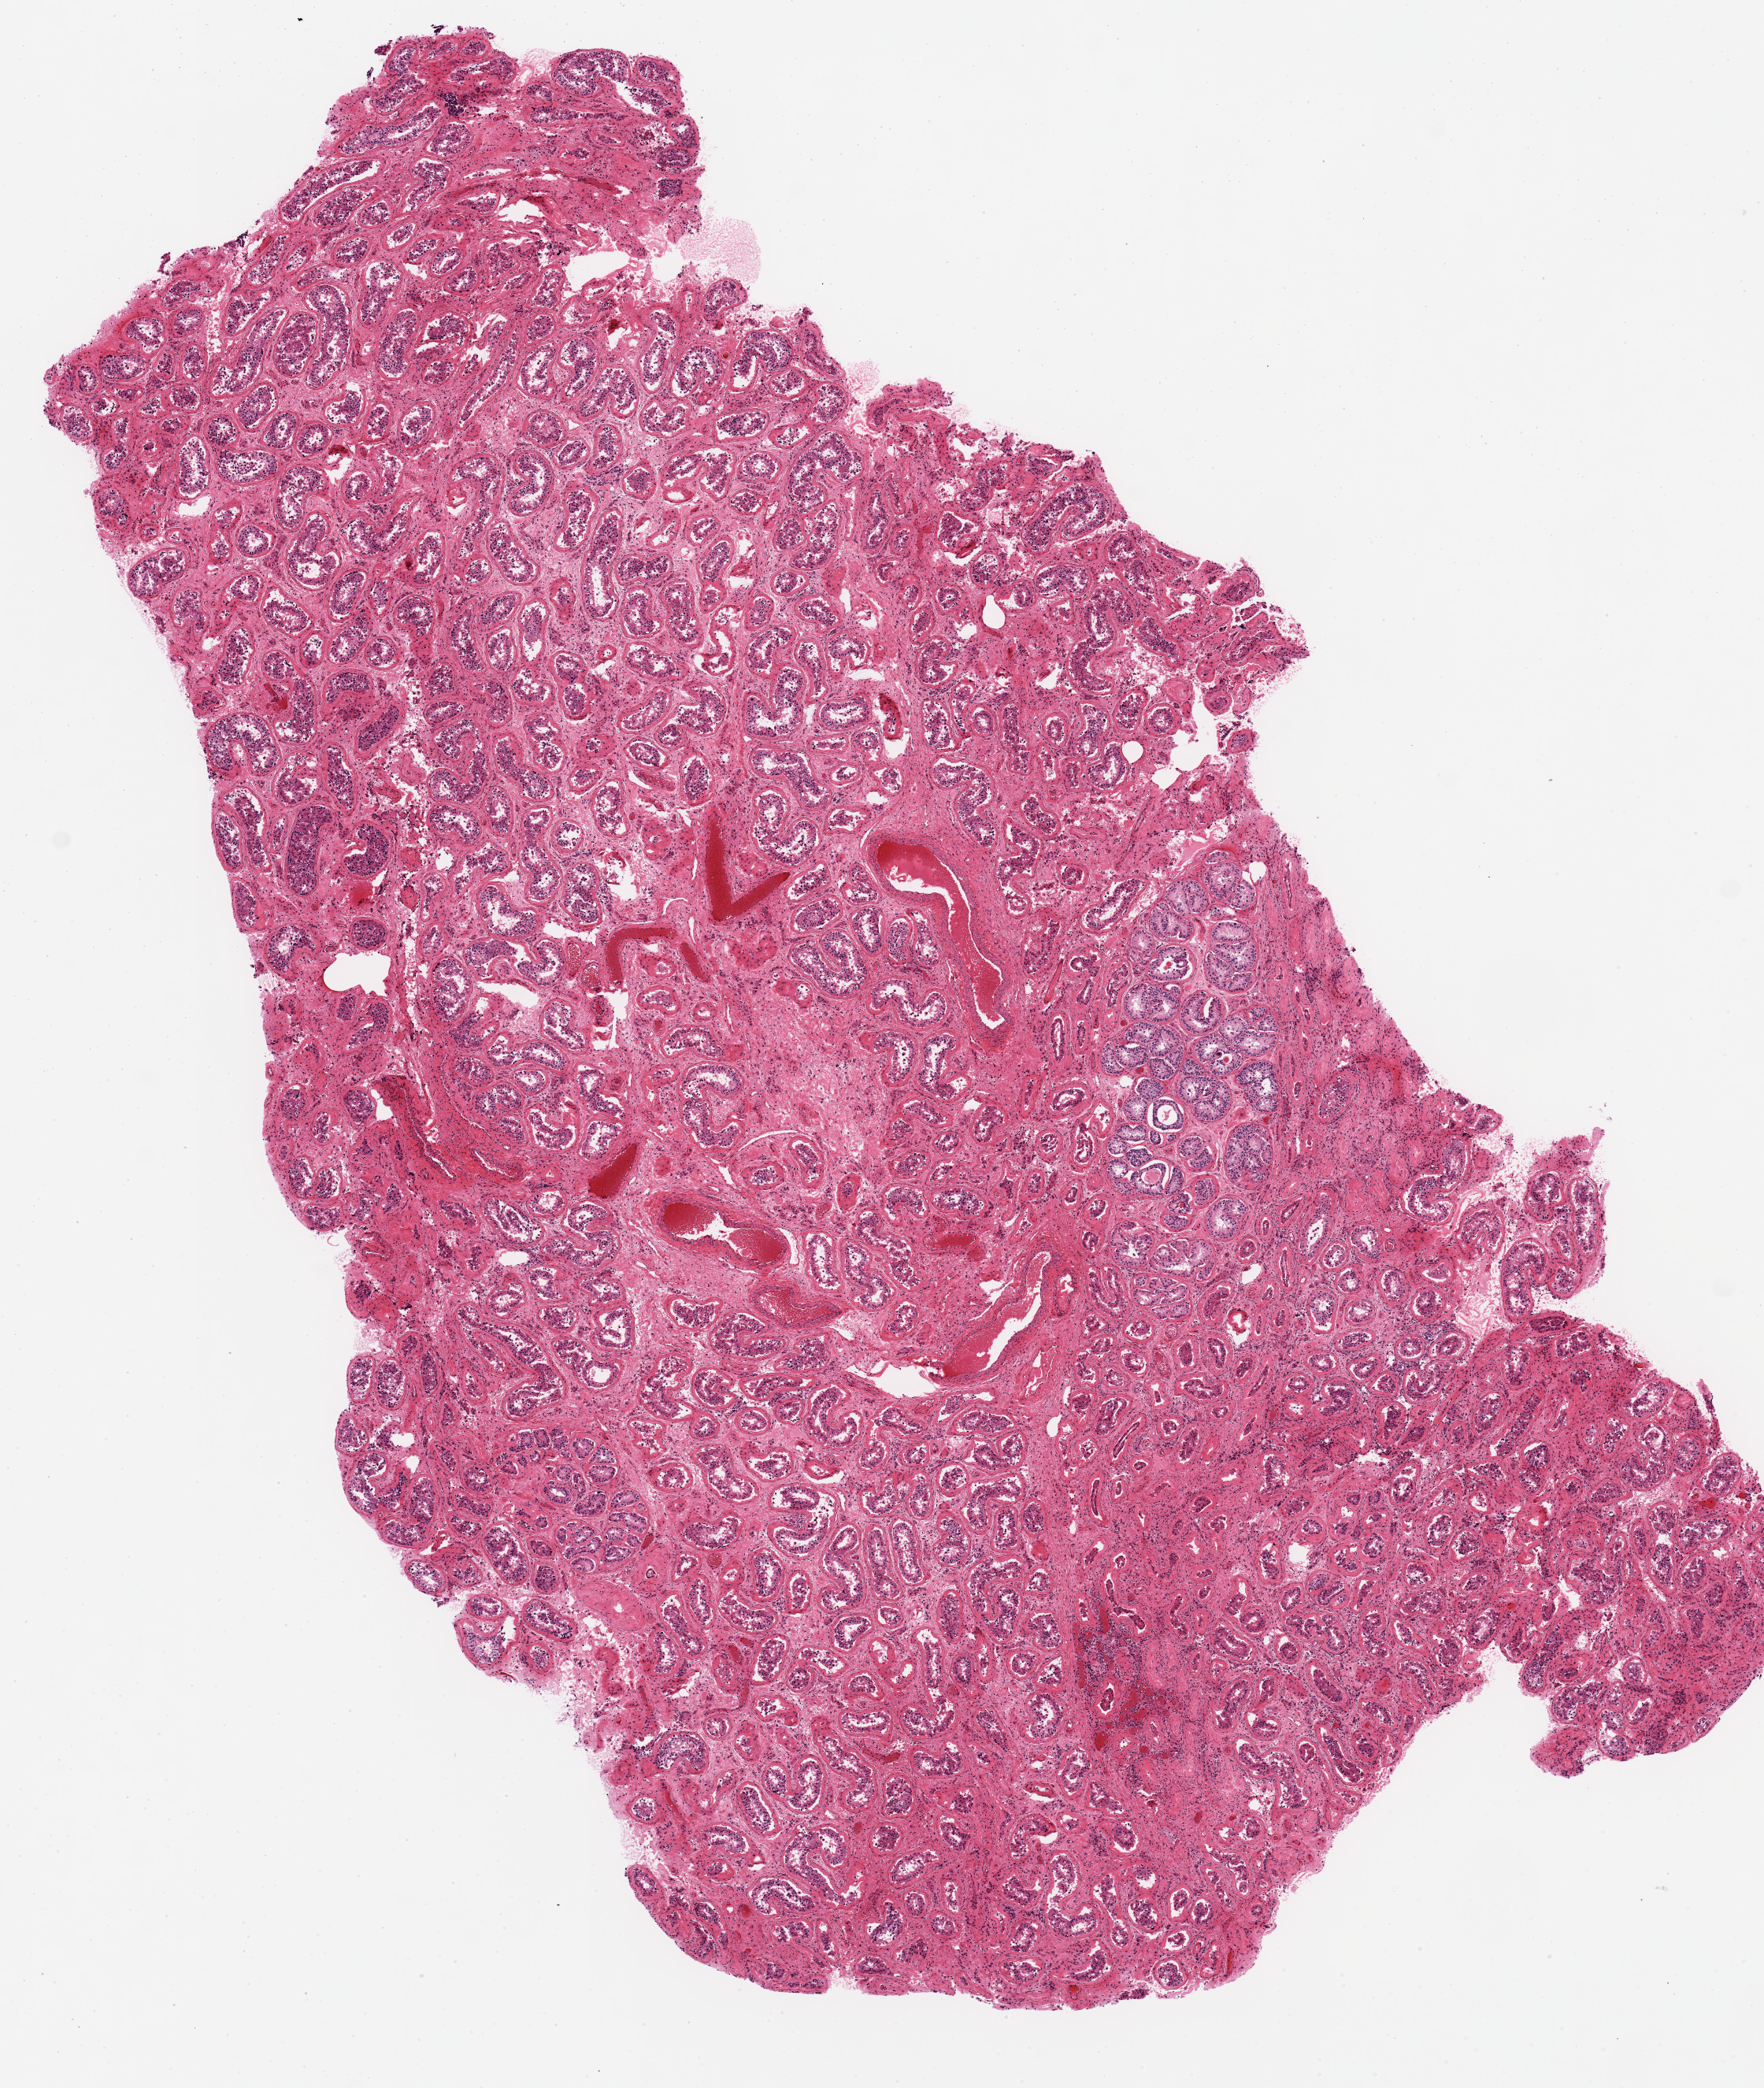
Whole-slide image, hematoxylin and eosin (H&E) stain — low-resolution overview of the scanned area, about 8.9 x 10.5 mm (from a 20x scan), PAXgene-fixed paraffin-embedded (PFPE) section, target tissue: testis, donor tissue sample. Male donor.
Pathologist's review note for this sample: 10x5.6mm. Maturational arrest evident.